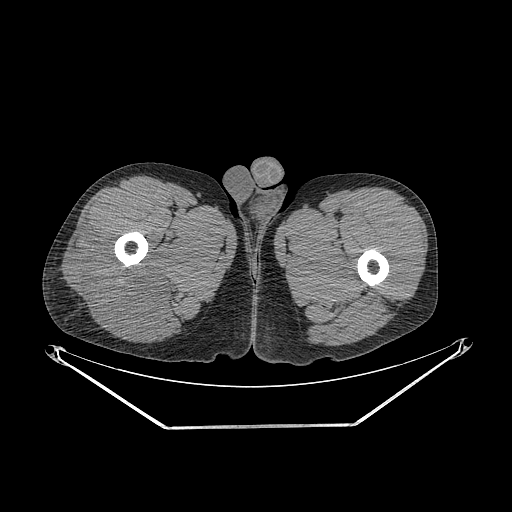
CT of an extremity soft-tissue mass (from a PET/CT study), one axial slice. Slice 267 of 267 in the series (ordered by position). 140 kVp. Soft-tissue window (W 400 / L 40 HU). 512 × 512 image matrix. Male patient. Case-level facts recorded for this patient, not image findings: histological type: poorly differentiated synovial sarcoma; grade: high; site of the primary tumour: right buttock.
Annotated regions visible in this slice (expert contour drawn on MRI and transferred to this co-registered scan by the dataset authors):
- gross tumour volume including surrounding oedema: bounding box (x1, y1, x2, y2) in pixels: (64, 231, 179, 334)
- gross tumour volume (mass): (64, 231, 165, 332)